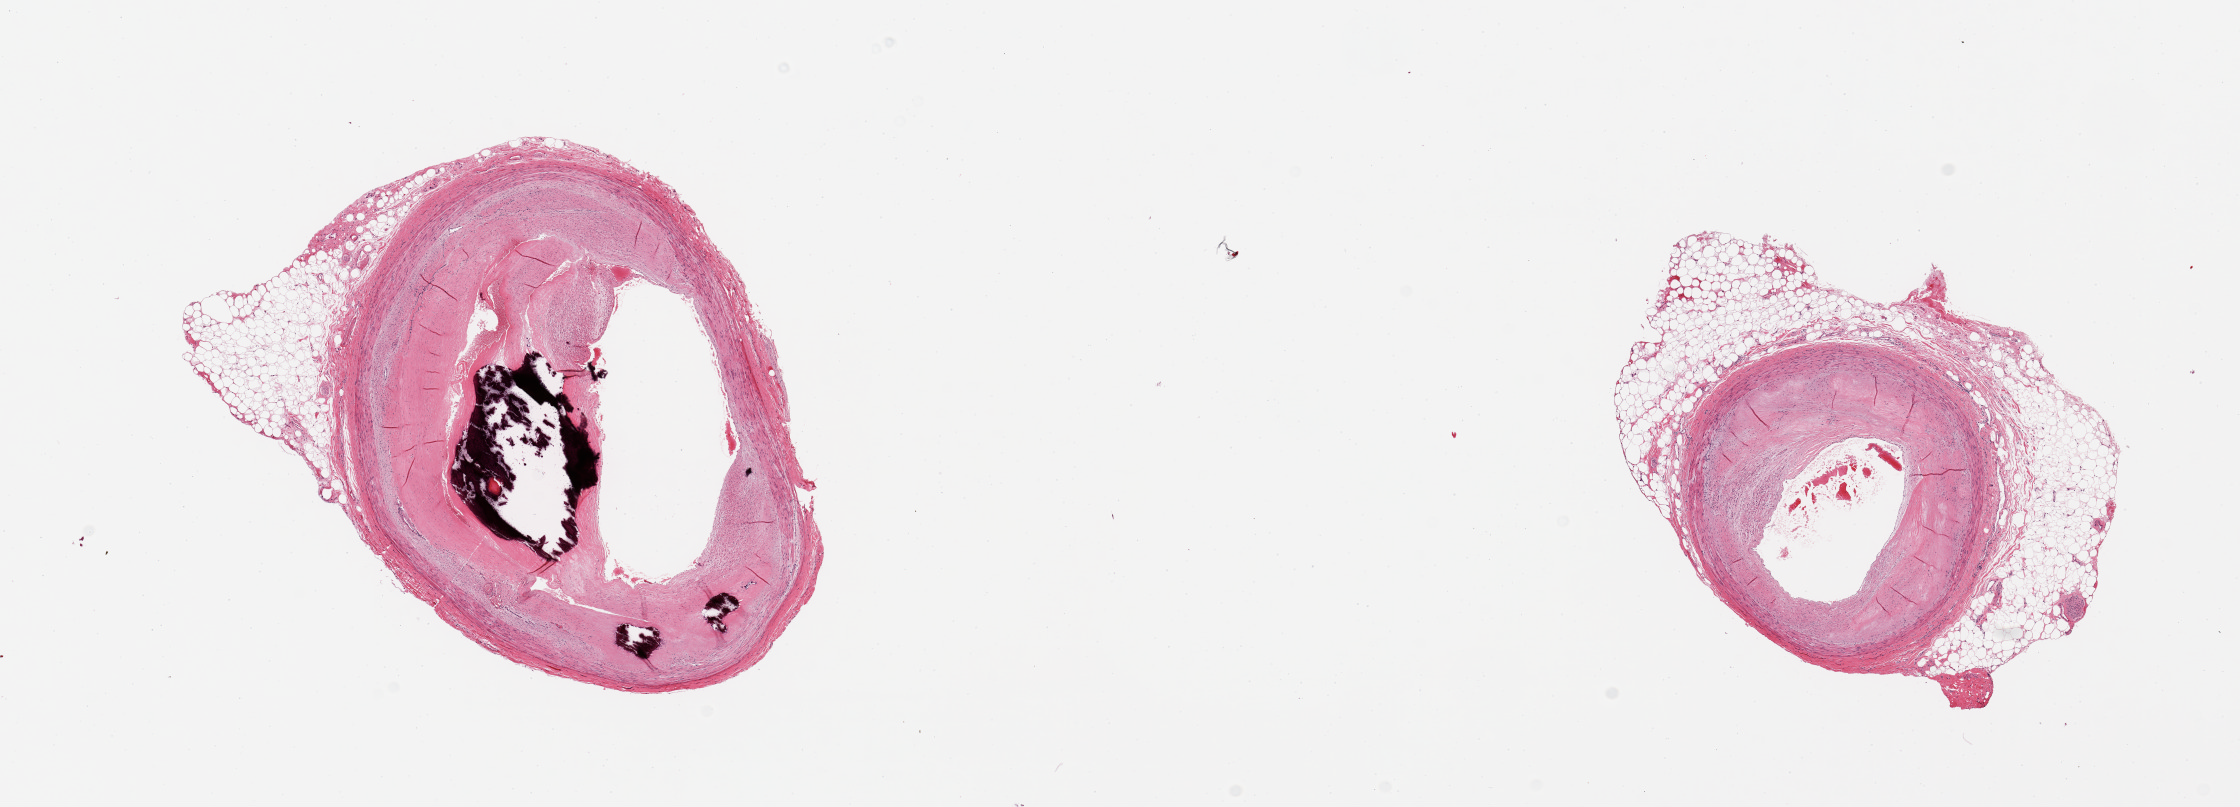
Whole-slide image, haematoxylin and eosin stain, brightfield — whole scanned area (about 17.7 x 6.4 mm, acquisition: 20x scan) shown as a low-resolution overview, PAXgene-fixed, paraffin-embedded tissue, section of coronary artery (target tissue), tissue donor sample. Donor: male.
Pathologist's review note for this sample: 2 pieces, ~70% occlusive focally calcified atherosis; Rim of adherent fat up to ~1mm.